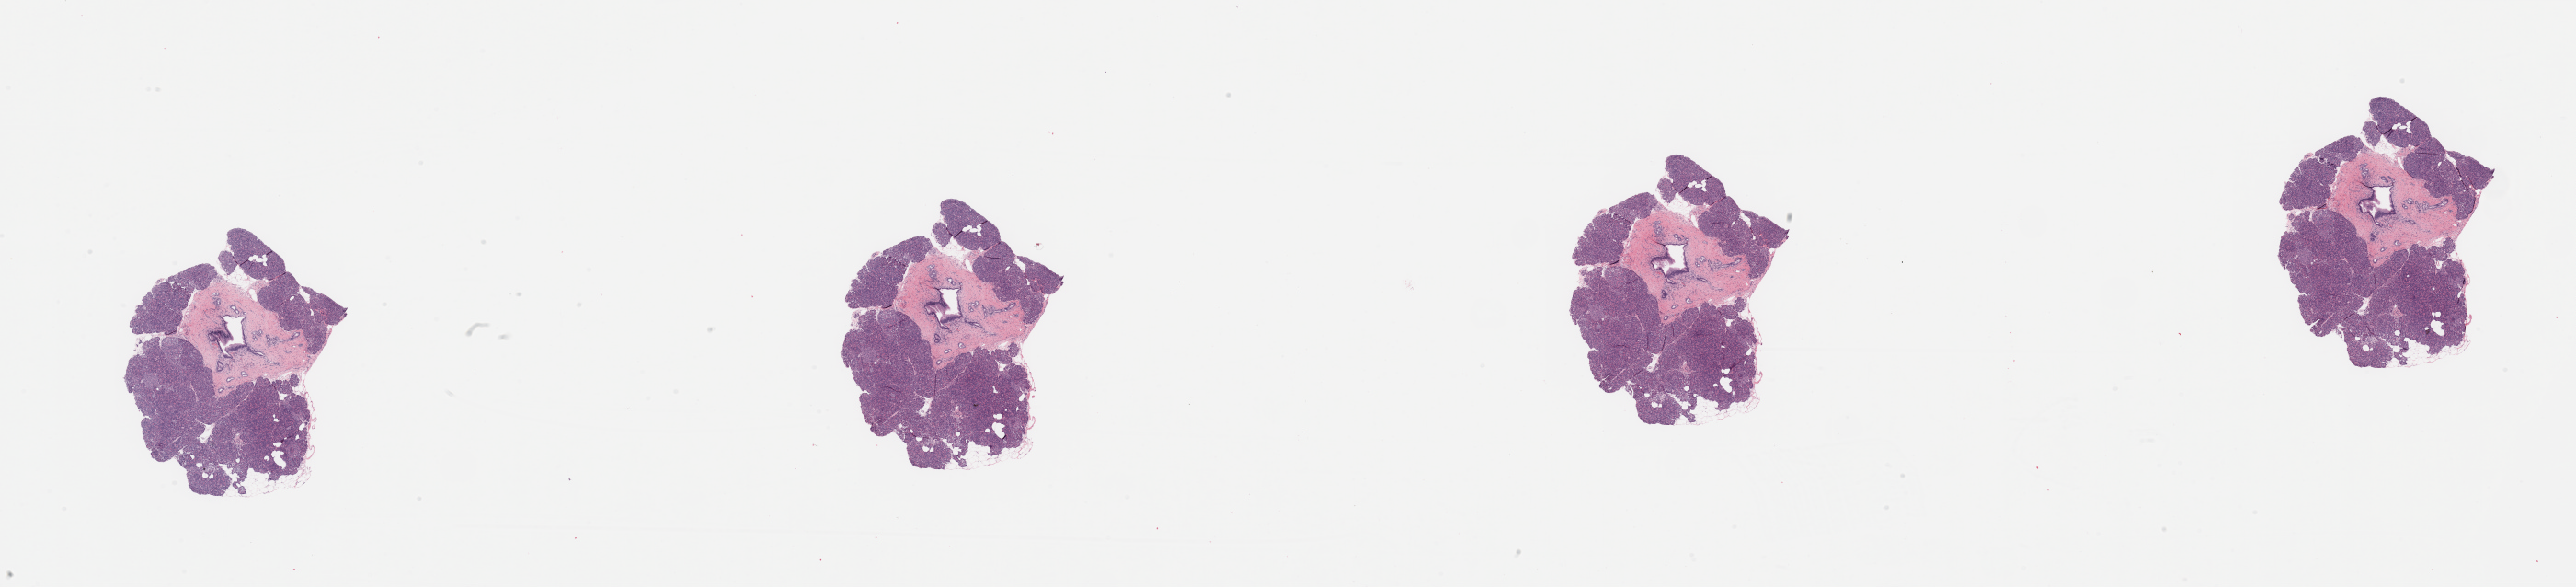
Digitized H&E-stained tissue section (whole slide) — whole scanned area (about 44.3 x 10.1 mm, slide scanned at 20x) shown as a low-resolution overview, normal (non-tumour) tissue sample, pancreas. Female, 68 y/o.
This section: normal (non-tumour) tissue from the same patient. Patient diagnosis: Infiltrating duct carcinoma, NOS.